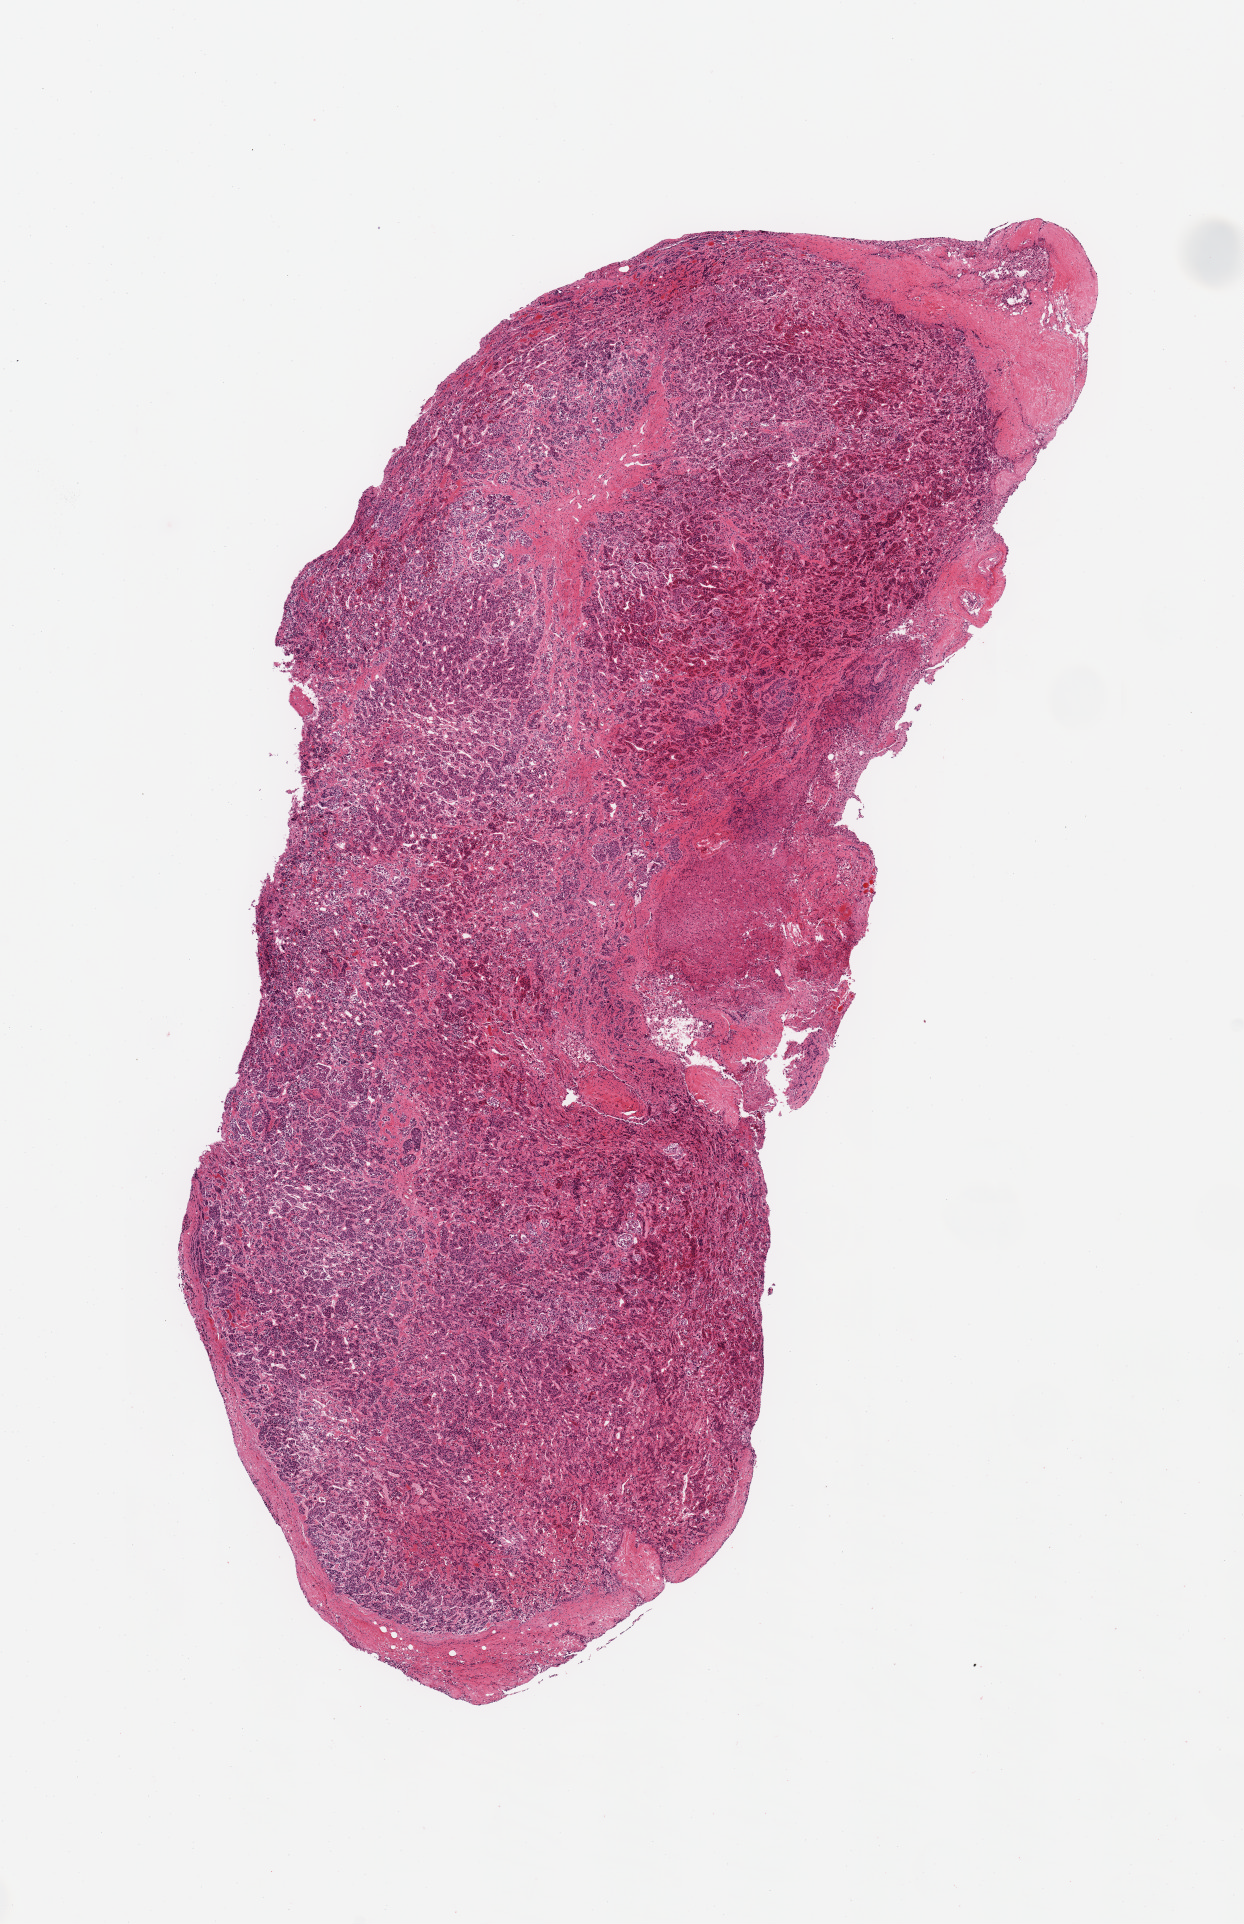
Whole-slide image, haematoxylin and eosin stain, shown as a low-resolution overview of the whole scanned area (about 9.8 x 15.2 mm), PAXgene-fixed, paraffin-embedded tissue, sampled site (target tissue): pituitary, donor tissue sample. Donor sex: male.
• pathologist's review note for this sample: 1 piece; mild to moderate autolysis, predominantly adenohypophysis